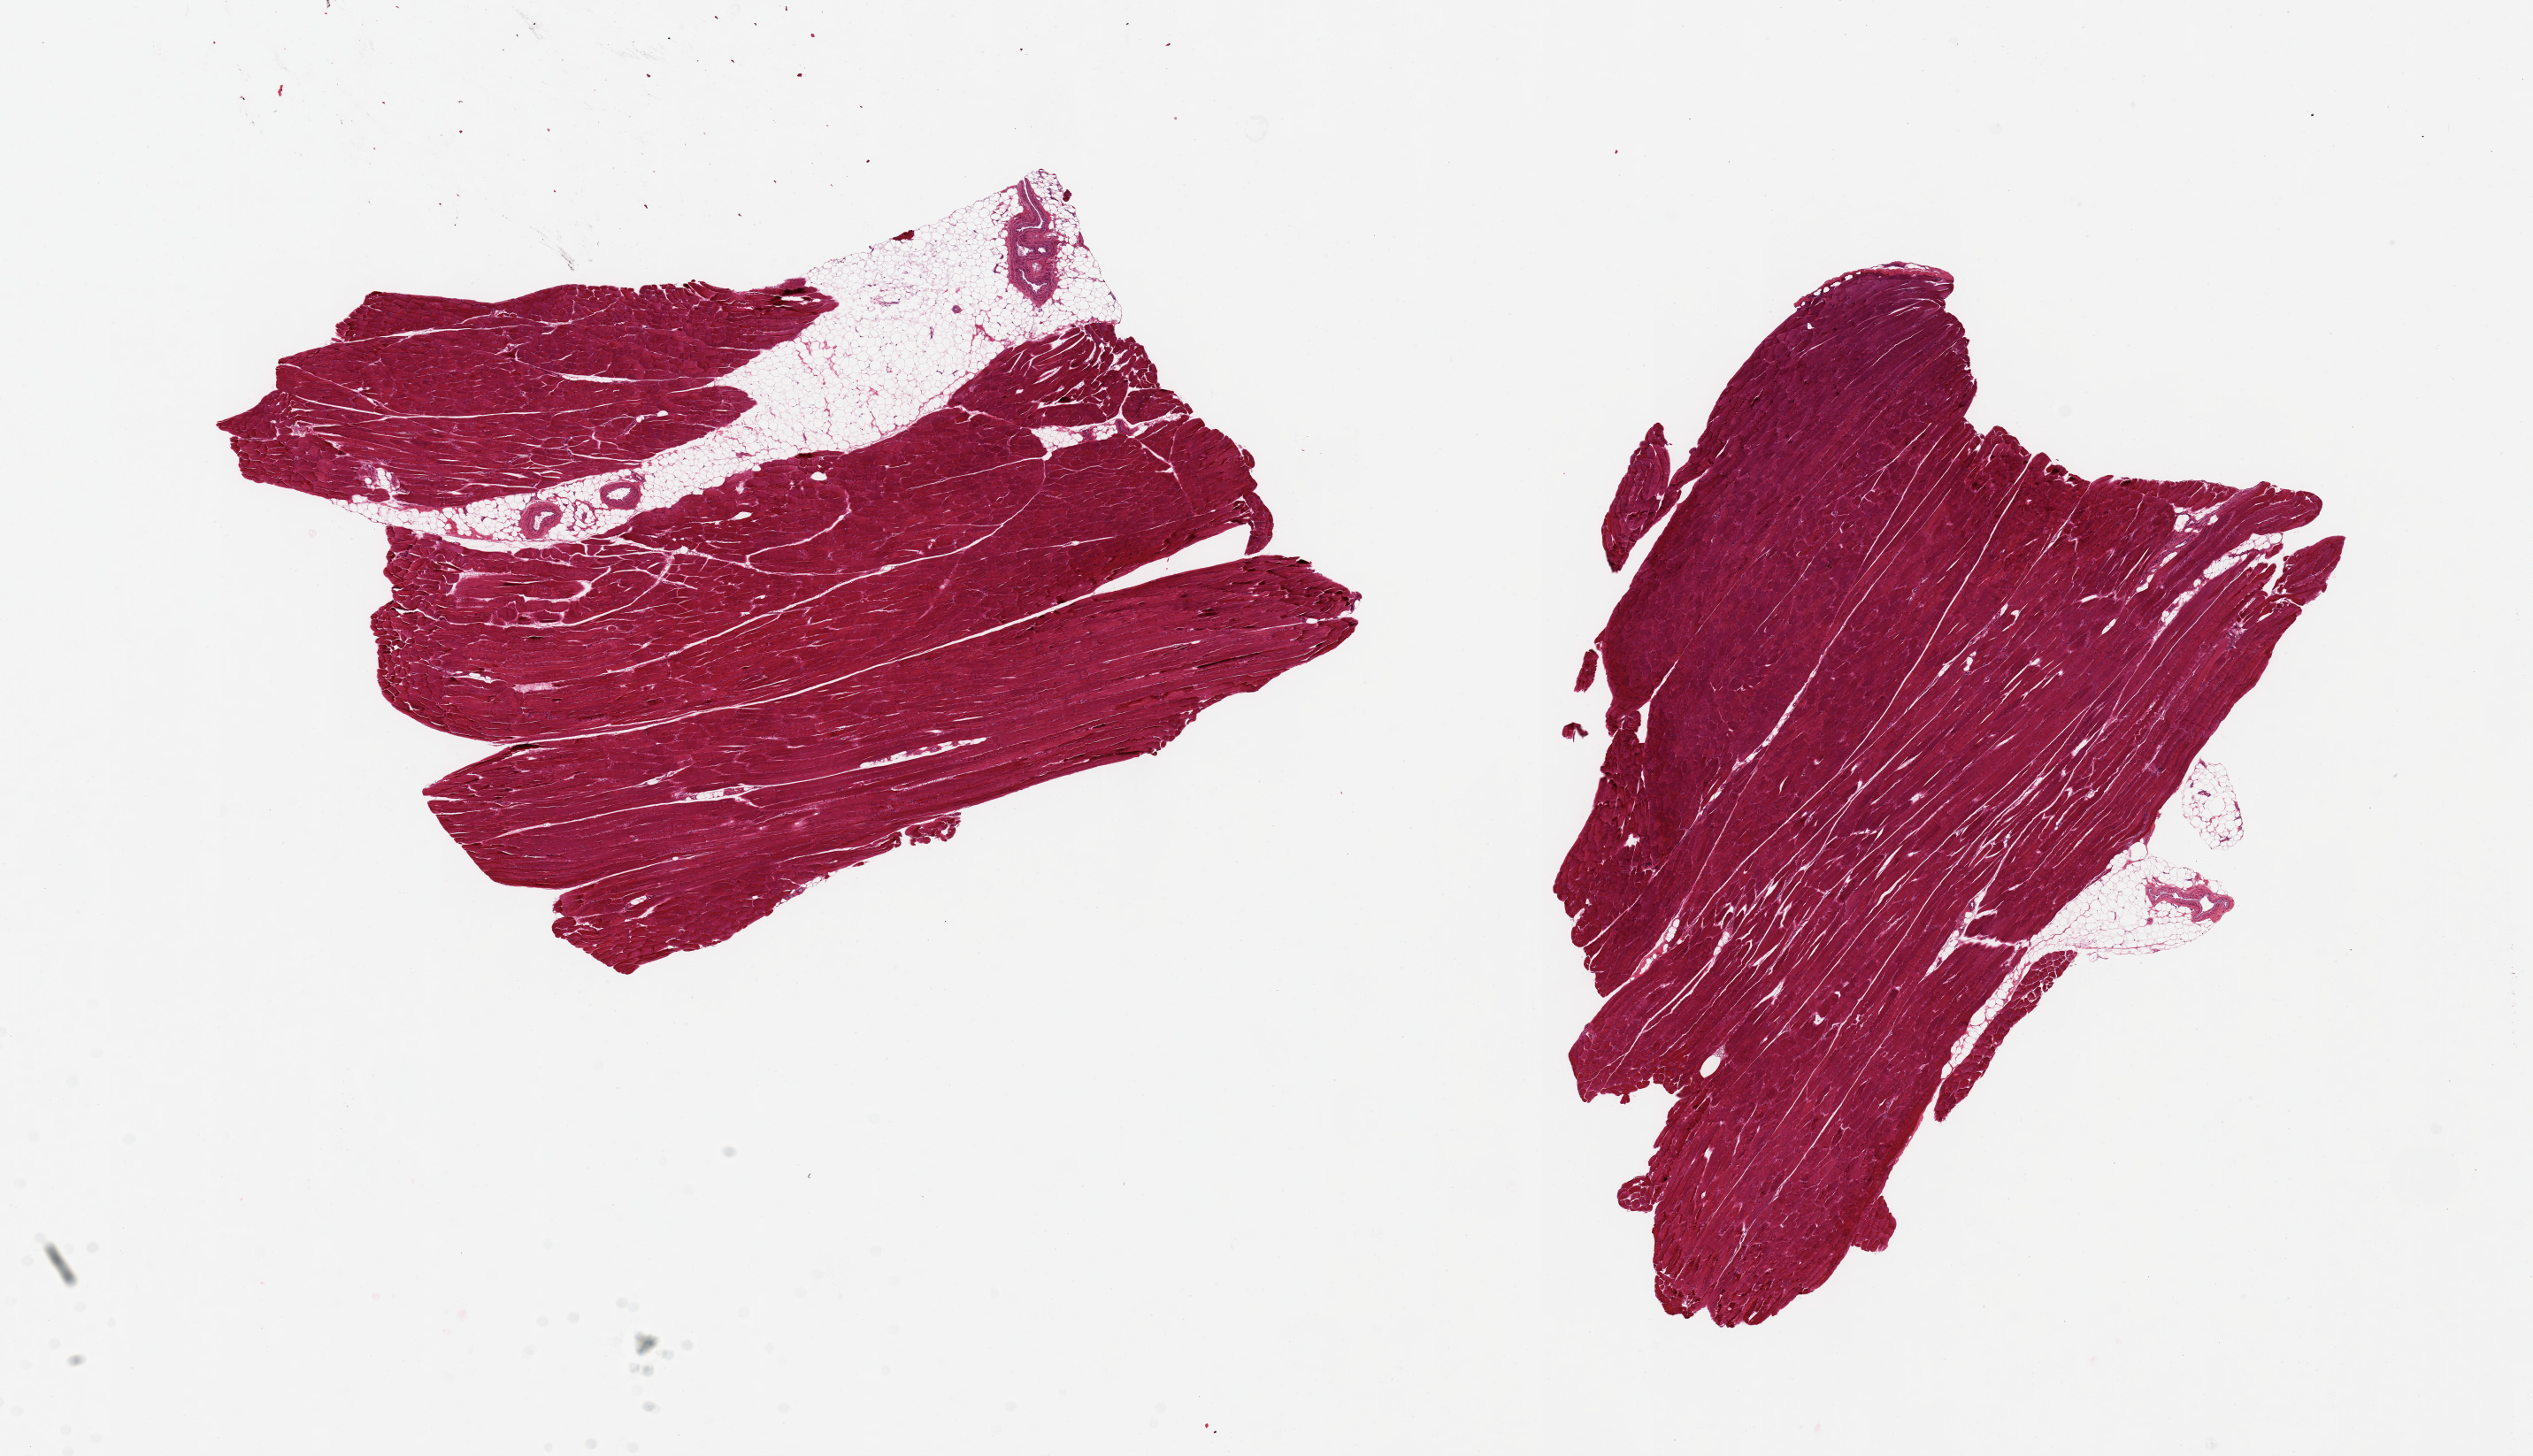
H&E whole-slide image — whole scanned area (about 22.6 x 13.0 mm) shown as a low-resolution overview. Donor sex: female.
Specimen: PAXgene-fixed paraffin-embedded (PFPE) section; sampled site (target tissue): skeletal muscle; tissue donor sample.